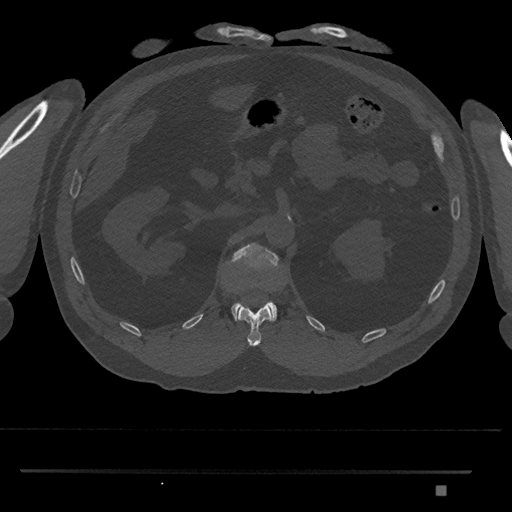
CT including the spine, one axial slice. Slice 859 of 1134 in the series (ordered by position). Bone window (W 1800 / L 400 HU). 512 × 512 image matrix. Patient: male, 65 years. Case-level facts recorded for this patient, not image findings: primary cancer: prostate.
Annotated regions visible in this slice (semi-automatically segmented with operator editing):
- L1 vertebra: bounding box <230,243,279,322> (left, top, right, bottom; pixels)
- T12 vertebra: <237,304,272,346>